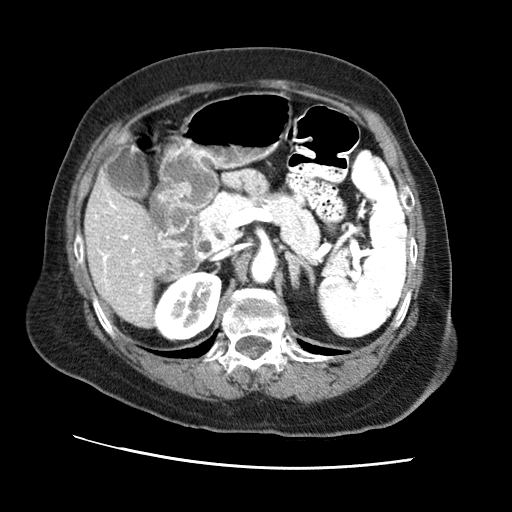
Contrast-enhanced abdominal CT (liver protocol), one axial slice; slice 28 of 65 in the series (ordered by position); reconstruction kernel STANDARD; 120 kVp; soft-tissue window (W 400 / L 40 HU); 512 × 512 image matrix, field of view 340 × 340 mm. From the clinical record (not read from this slice): diagnosis: hepatocellular carcinoma (patient treated with transarterial chemoembolisation; whether this scan precedes or follows treatment is not stated here); TNM stage (as recorded): Stage-II; Child-Pugh class: A; tumour differentiation: no biopsy.
Annotated regions visible in this slice (semi-automatic segmentation, software-assisted and operator-edited):
- liver parenchyma outside the tumour (the mass and vessels are separate outlines, so this box may not span the whole liver): bounding box <84,146,168,326> (left, top, right, bottom; pixels)
- liver vessels: <95,192,148,308>